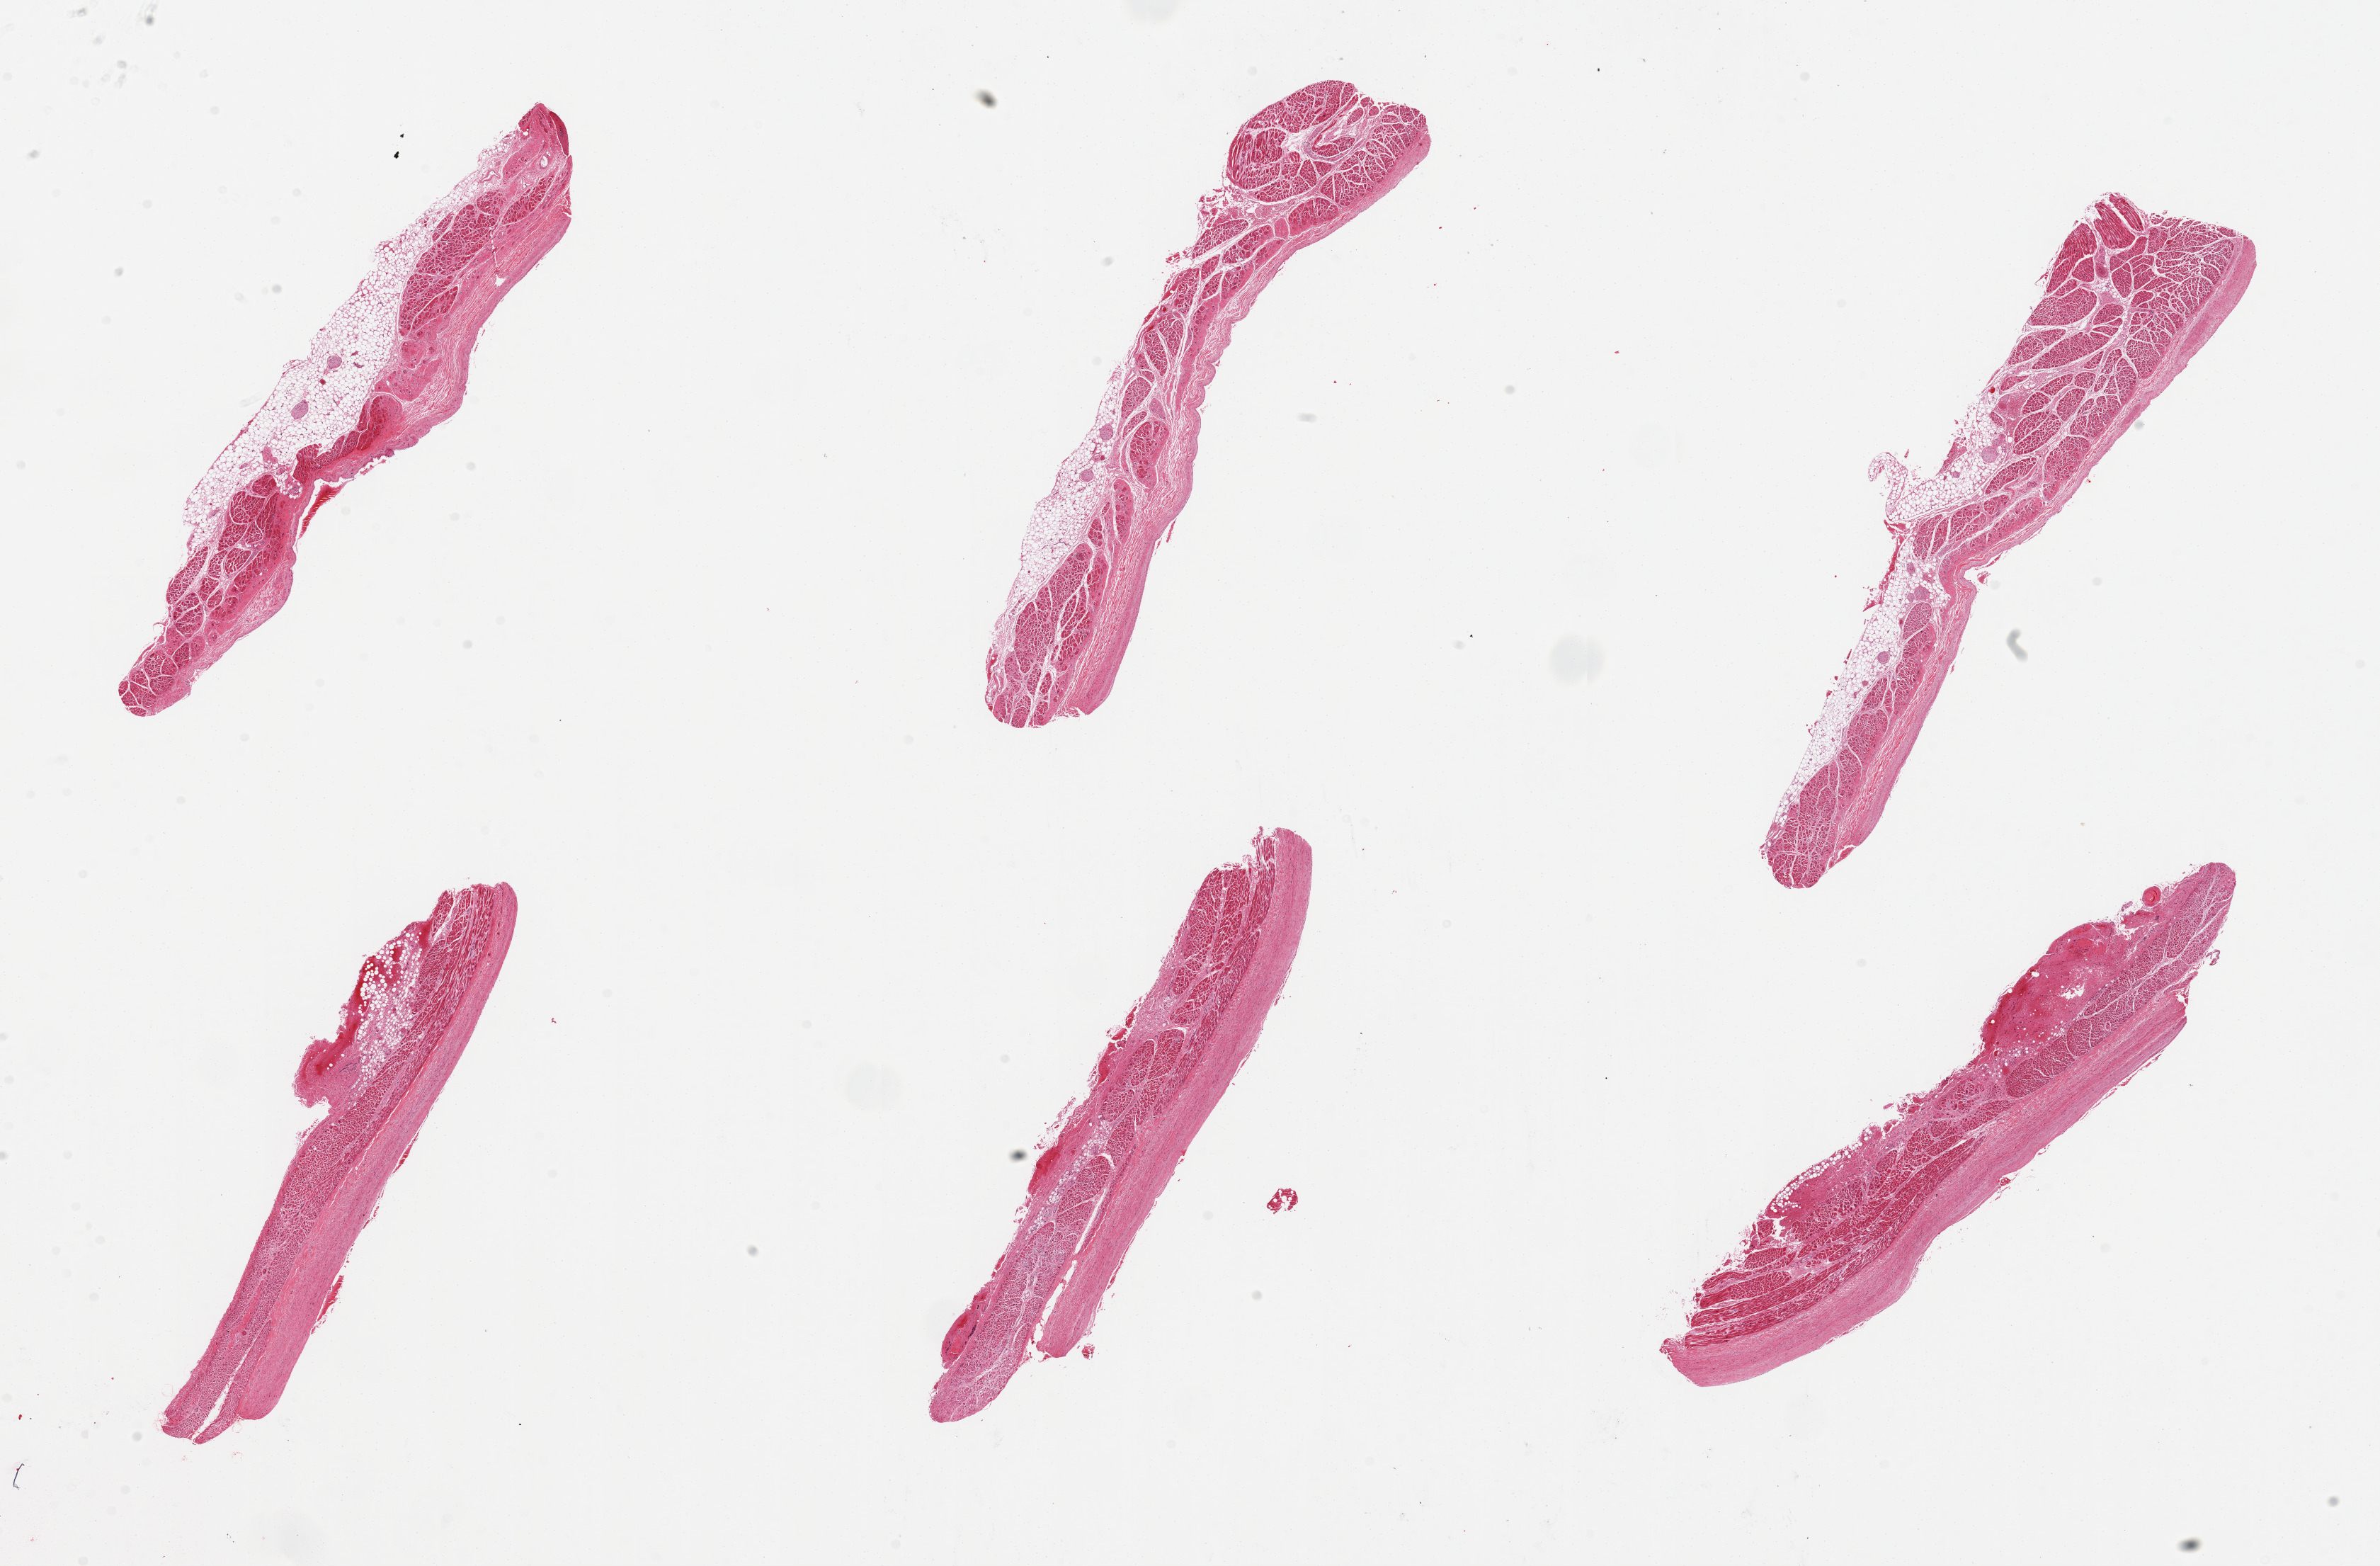
Digitized hematoxylin and eosin (H&E)-stained section, brightfield, a low-resolution overview of the entire scanned area, about 26.6 x 17.5 mm, PAXgene-fixed, paraffin-embedded tissue, sampled site (target tissue): aorta, tissue donor sample. Donor: male.
Reviewer comment on this tissue sample: 6 pieces; NOT aorta, probably pulmonary vein with surrounding cardiac muscle.